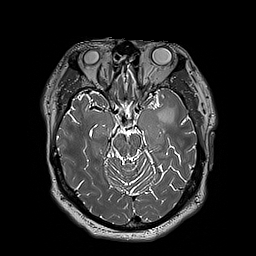
Brain MRI from a brain-tumour surgery series, one axial slice; slice 123 of 192 in the series (ordered by position); 1 mm slice thickness; 256 × 256 image matrix, field of view 250 × 250 mm. From the clinical record (not read from this slice): histopathology: Astrocytoma; WHO grade: 3; IDH mutation: yes; tumour location: Left Insular.
Annotated regions visible in this slice (manually delineated by an expert):
- tumour: box from (x=155, y=106) to (x=174, y=123) px